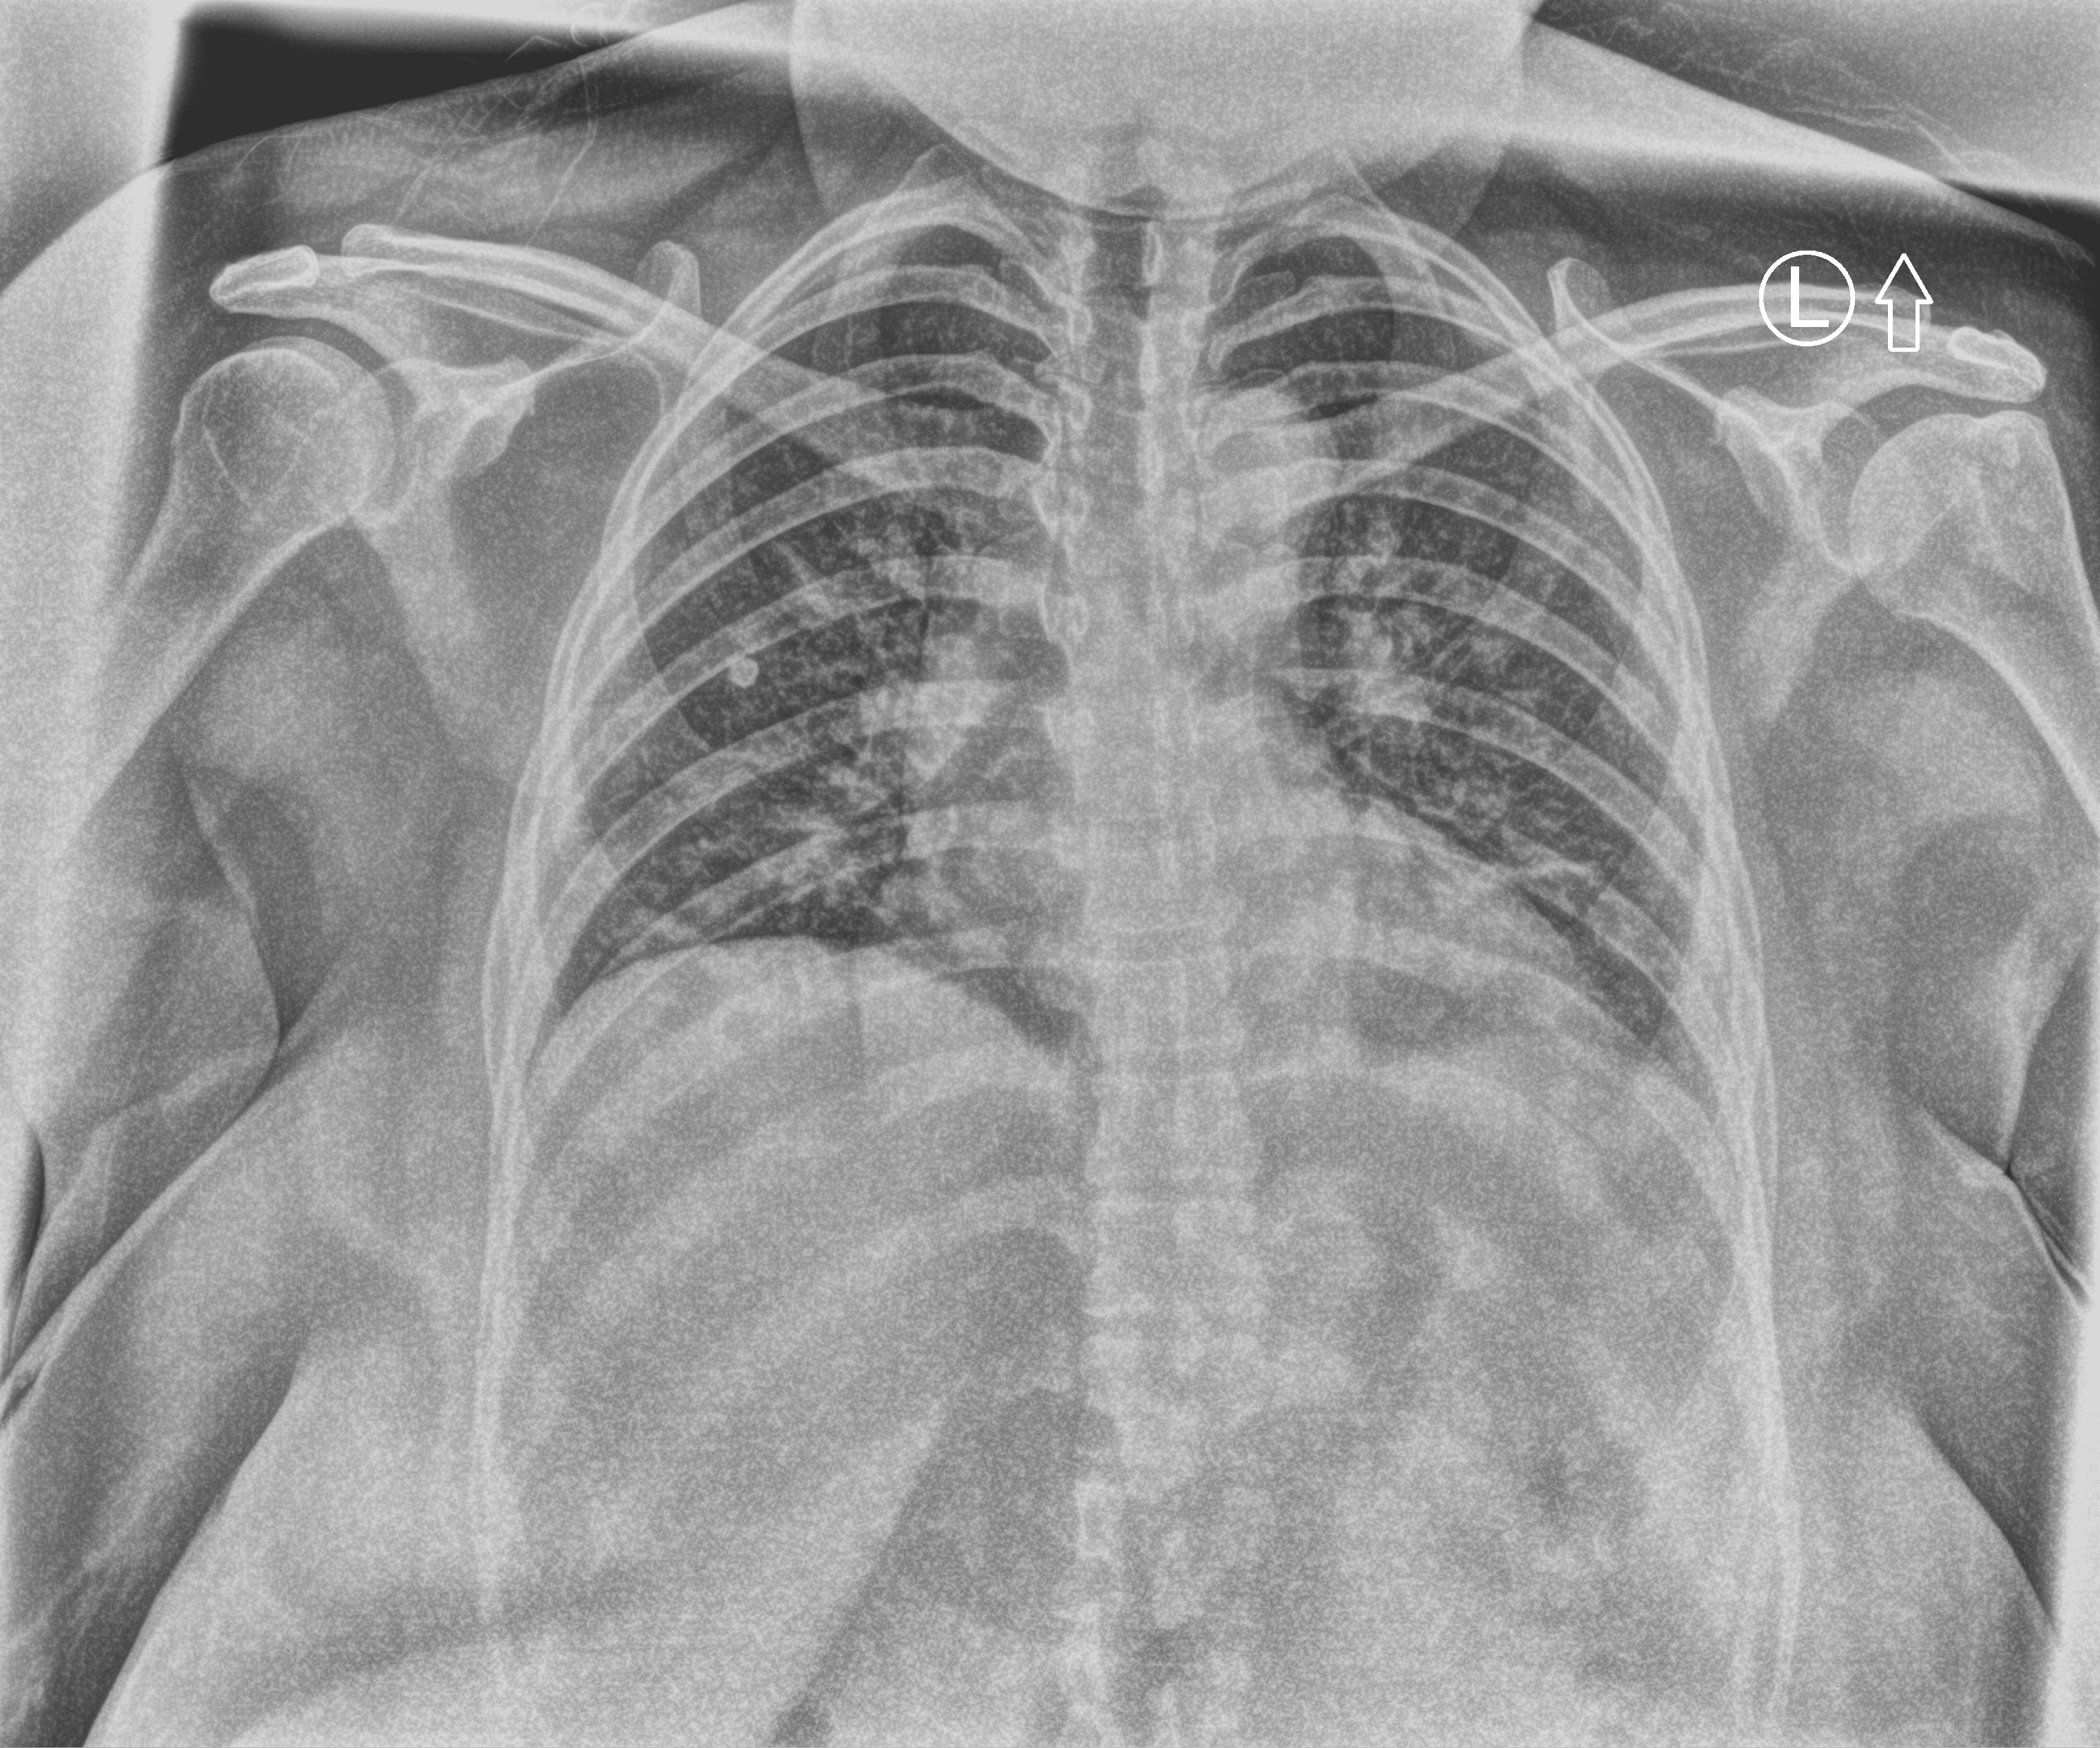
Portable chest radiograph, anteroposterior (AP) projection. Patient hospitalised with COVID-19; female, aged 18–59 years.
From the hospital-stay record, not from the radiograph (when in the stay this image was taken is not recorded): mechanically ventilated during this hospital stay: no; hypertension (admission record): no.